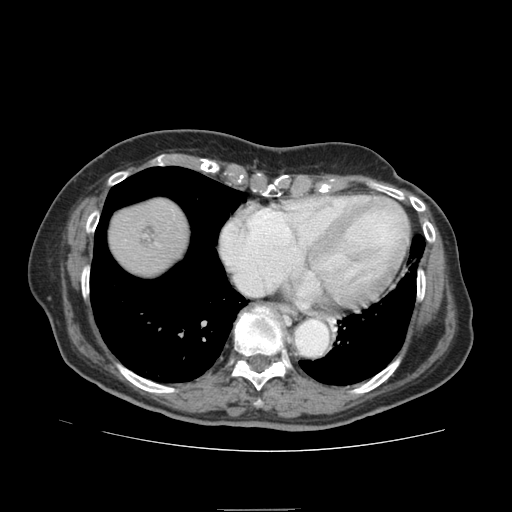
Contrast-enhanced abdominal CT (liver protocol), one axial slice; position 79 of 95 along the scan axis; 140 kVp; soft-tissue window (W 400 / L 40 HU); 2.5 mm slice thickness; 512 × 512 image matrix. Case-level facts recorded for this patient, not image findings: diagnosis: hepatocellular carcinoma (patient treated with transarterial chemoembolisation; whether this scan precedes or follows treatment is not stated here); TNM stage (as recorded): Stage-IVA; Child-Pugh class: B; tumour nodularity: uninodular.
Annotated regions visible in this slice (semi-automatically segmented with operator editing):
- abdominal aorta: bounding box [x1, y1, x2, y2] px = [296, 319, 327, 354]
- liver parenchyma outside the tumour (the mass and vessels are separate outlines, so this box may not span the whole liver): [108, 198, 188, 274]